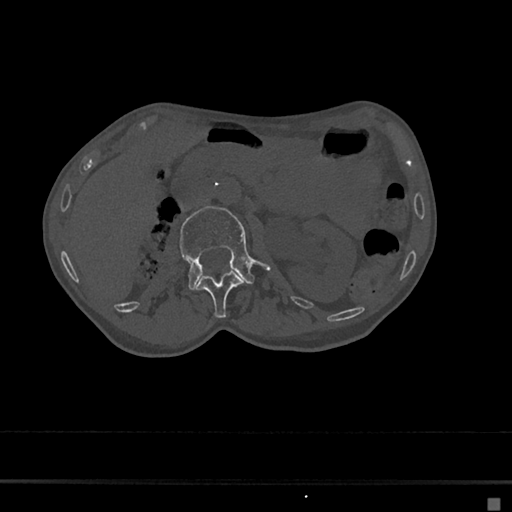
CT including the spine, one axial slice; position 38 of 797 along the scan axis; 120 kVp; bone window (W 1800 / L 400 HU); 0.5 mm slice thickness; 512 × 512 image matrix, field of view 360 × 360 mm. Female patient, age 68 years. From the clinical record (not read from this slice): primary cancer: renal.
Annotated regions visible in this slice (semi-automatic segmentation, software-assisted and operator-edited):
- L1 vertebra: box from (x=196, y=271) to (x=243, y=319) px
- L2 vertebra: (x=179, y=206)–(x=269, y=289)